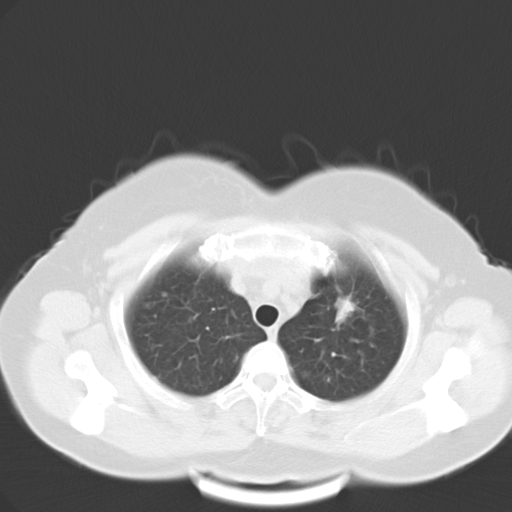
Chest CT, one axial slice. Position 23 of 28 along the scan axis. Reconstruction kernel B40f. 120 kVp. Lung window (W 1500 / L -600 HU). 10 mm slice thickness. 512 × 512 image matrix. Patient: female, 53 years. From the clinical record (not read from this slice): clinical TNM (as recorded): T1c N0 M1a.
Structures marked on this image (rectangle marked by the reading radiologist):
- lung tumour (recorded histology: adenocarcinoma): bounding box (x1, y1, x2, y2) in pixels: (328, 293, 355, 326)